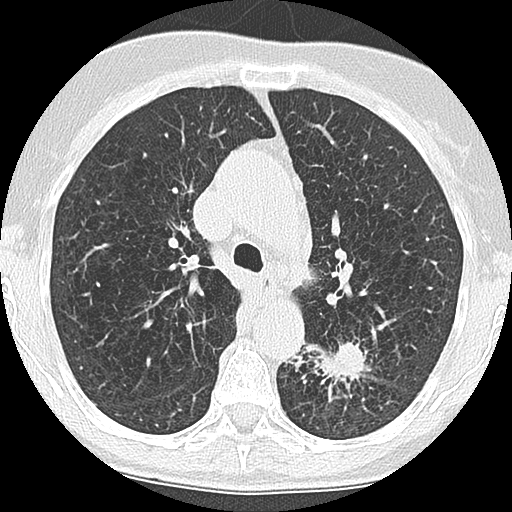
Low-dose screening chest CT, one axial slice. Position 120 of 171 along the scan axis. Reconstruction kernel LUNG. 120 kVp. Lung window (W 1500 / L -600 HU). 512 × 512 image matrix, field of view 280 × 280 mm.
Annotated regions visible in this slice (outlined manually by an expert reader):
- lesion 1 (tumor, lower lobe of left lung): box from (x=289, y=342) to (x=371, y=381) px